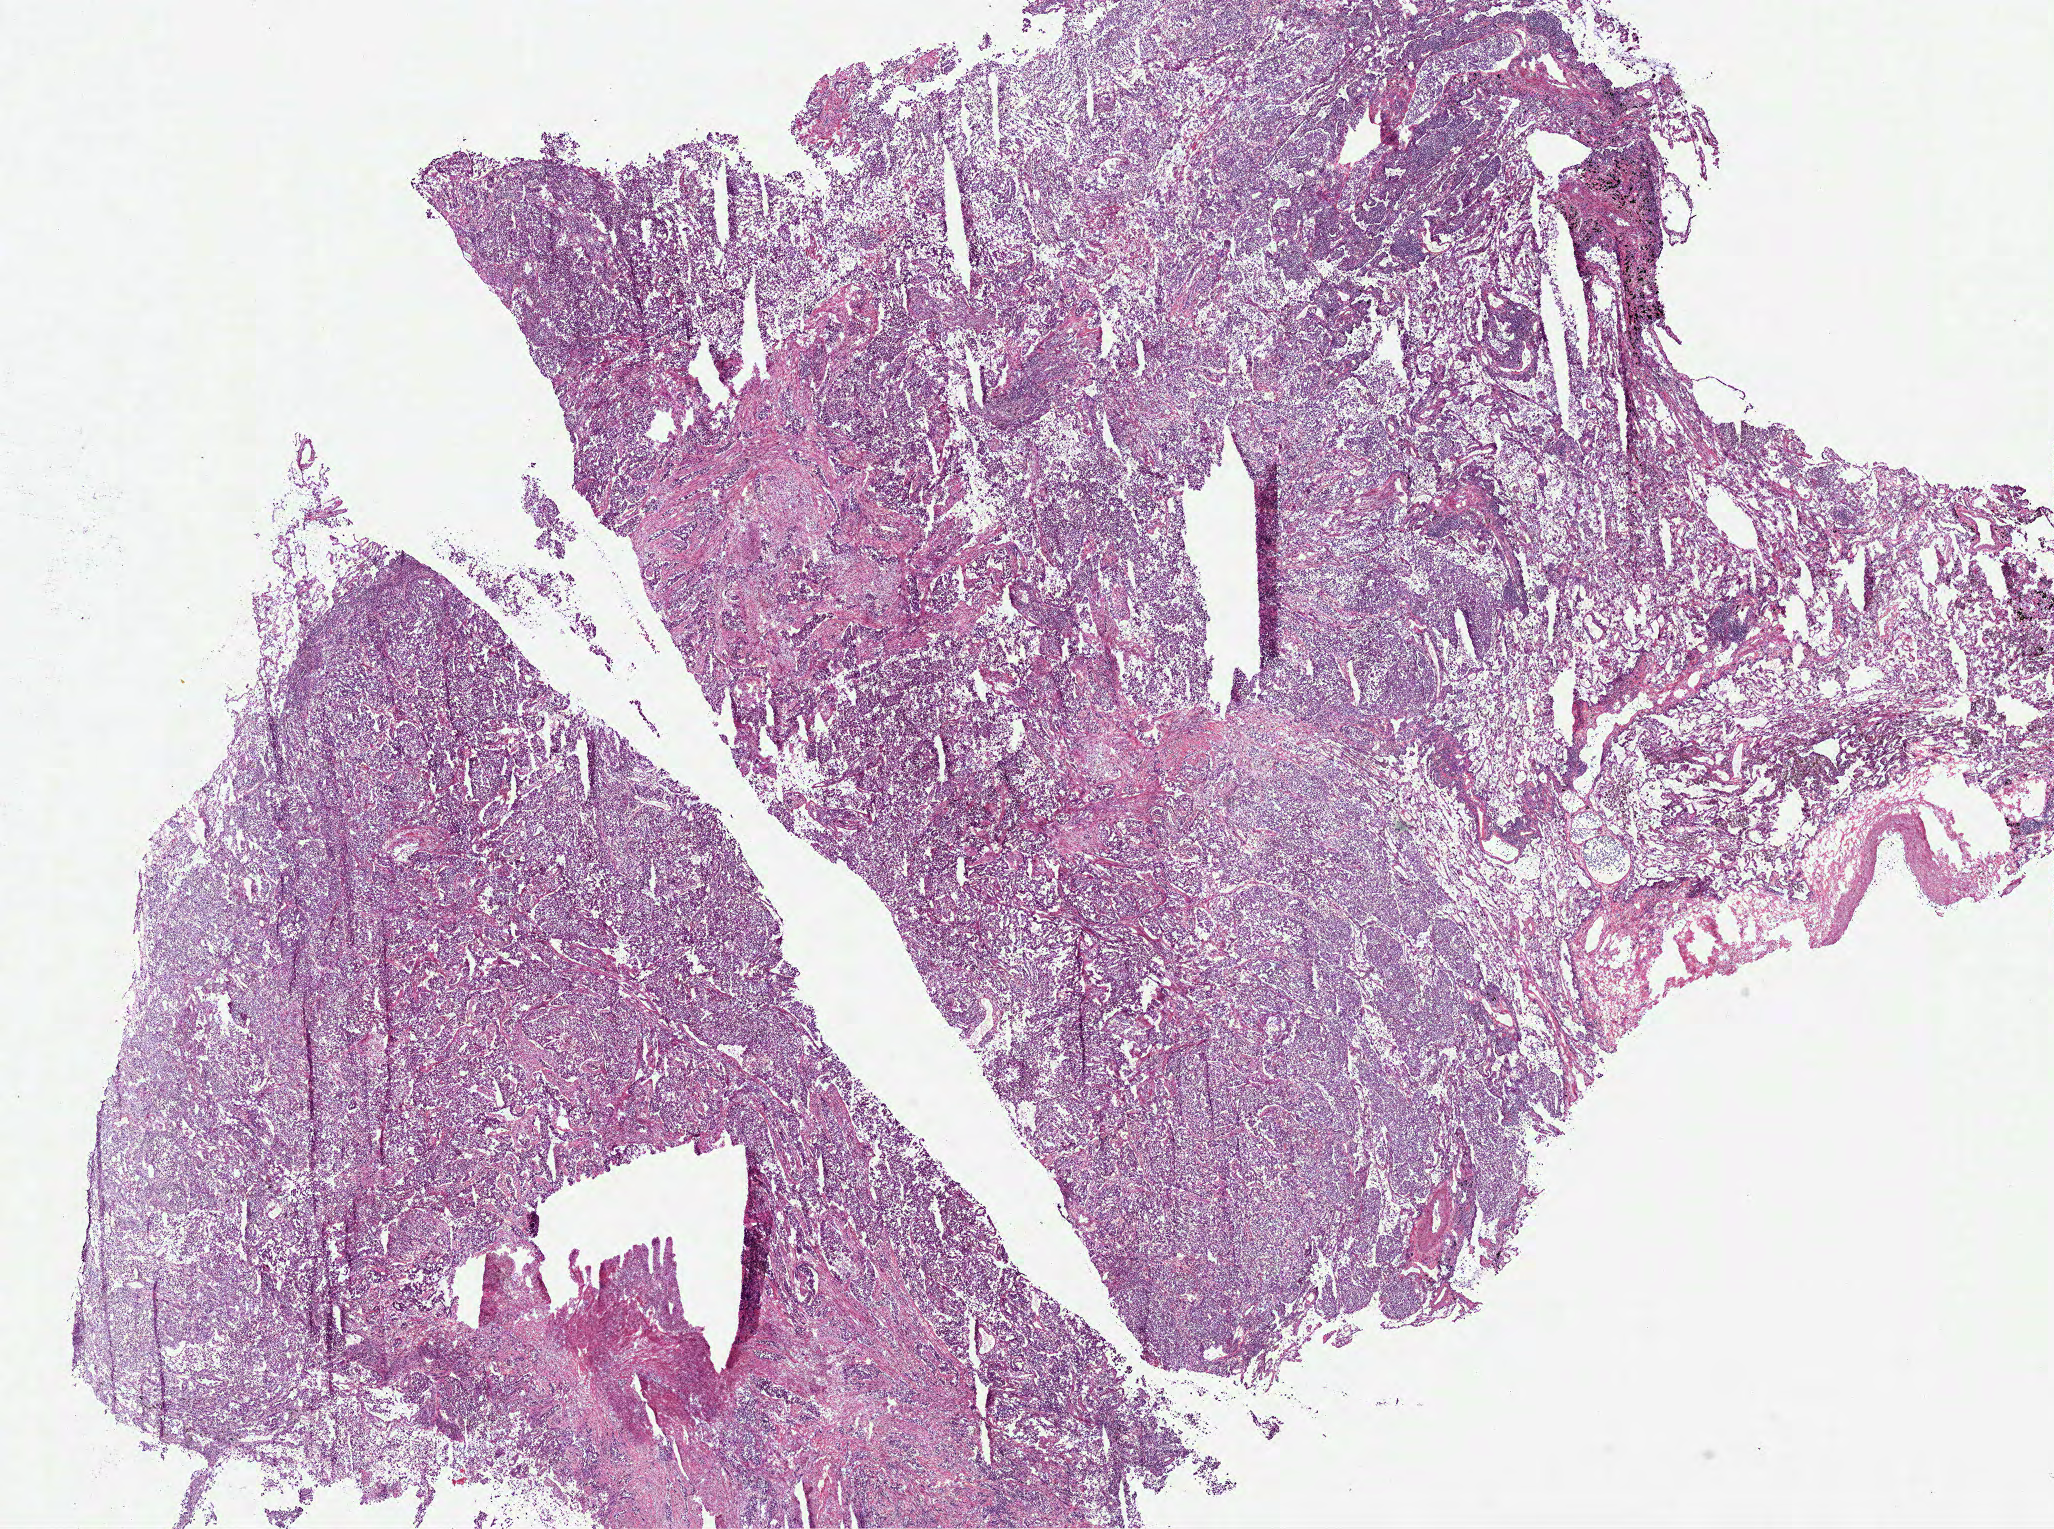
Digitized H&E tissue section (whole slide), low-resolution overview of the scanned area, about 16.6 x 12.3 mm (acquisition: 40x scan); frozen section from the top of the tissue portion; sample: primary tumour, lung. Male patient; age at initial diagnosis 62 years. Pathologist review of this section (percent, as recorded): tumour cells 73%, tumour nuclei 80%, normal cells 19%, stromal cells 0%, necrosis 8%. Infiltration values recorded for this section: lymphocyte infiltration 5%, monocyte infiltration 10%, neutrophil infiltration 1%.
Histologic diagnosis: Adenocarcinoma with mixed subtypes (upper lobe, lung). AJCC pathologic stage: IA.